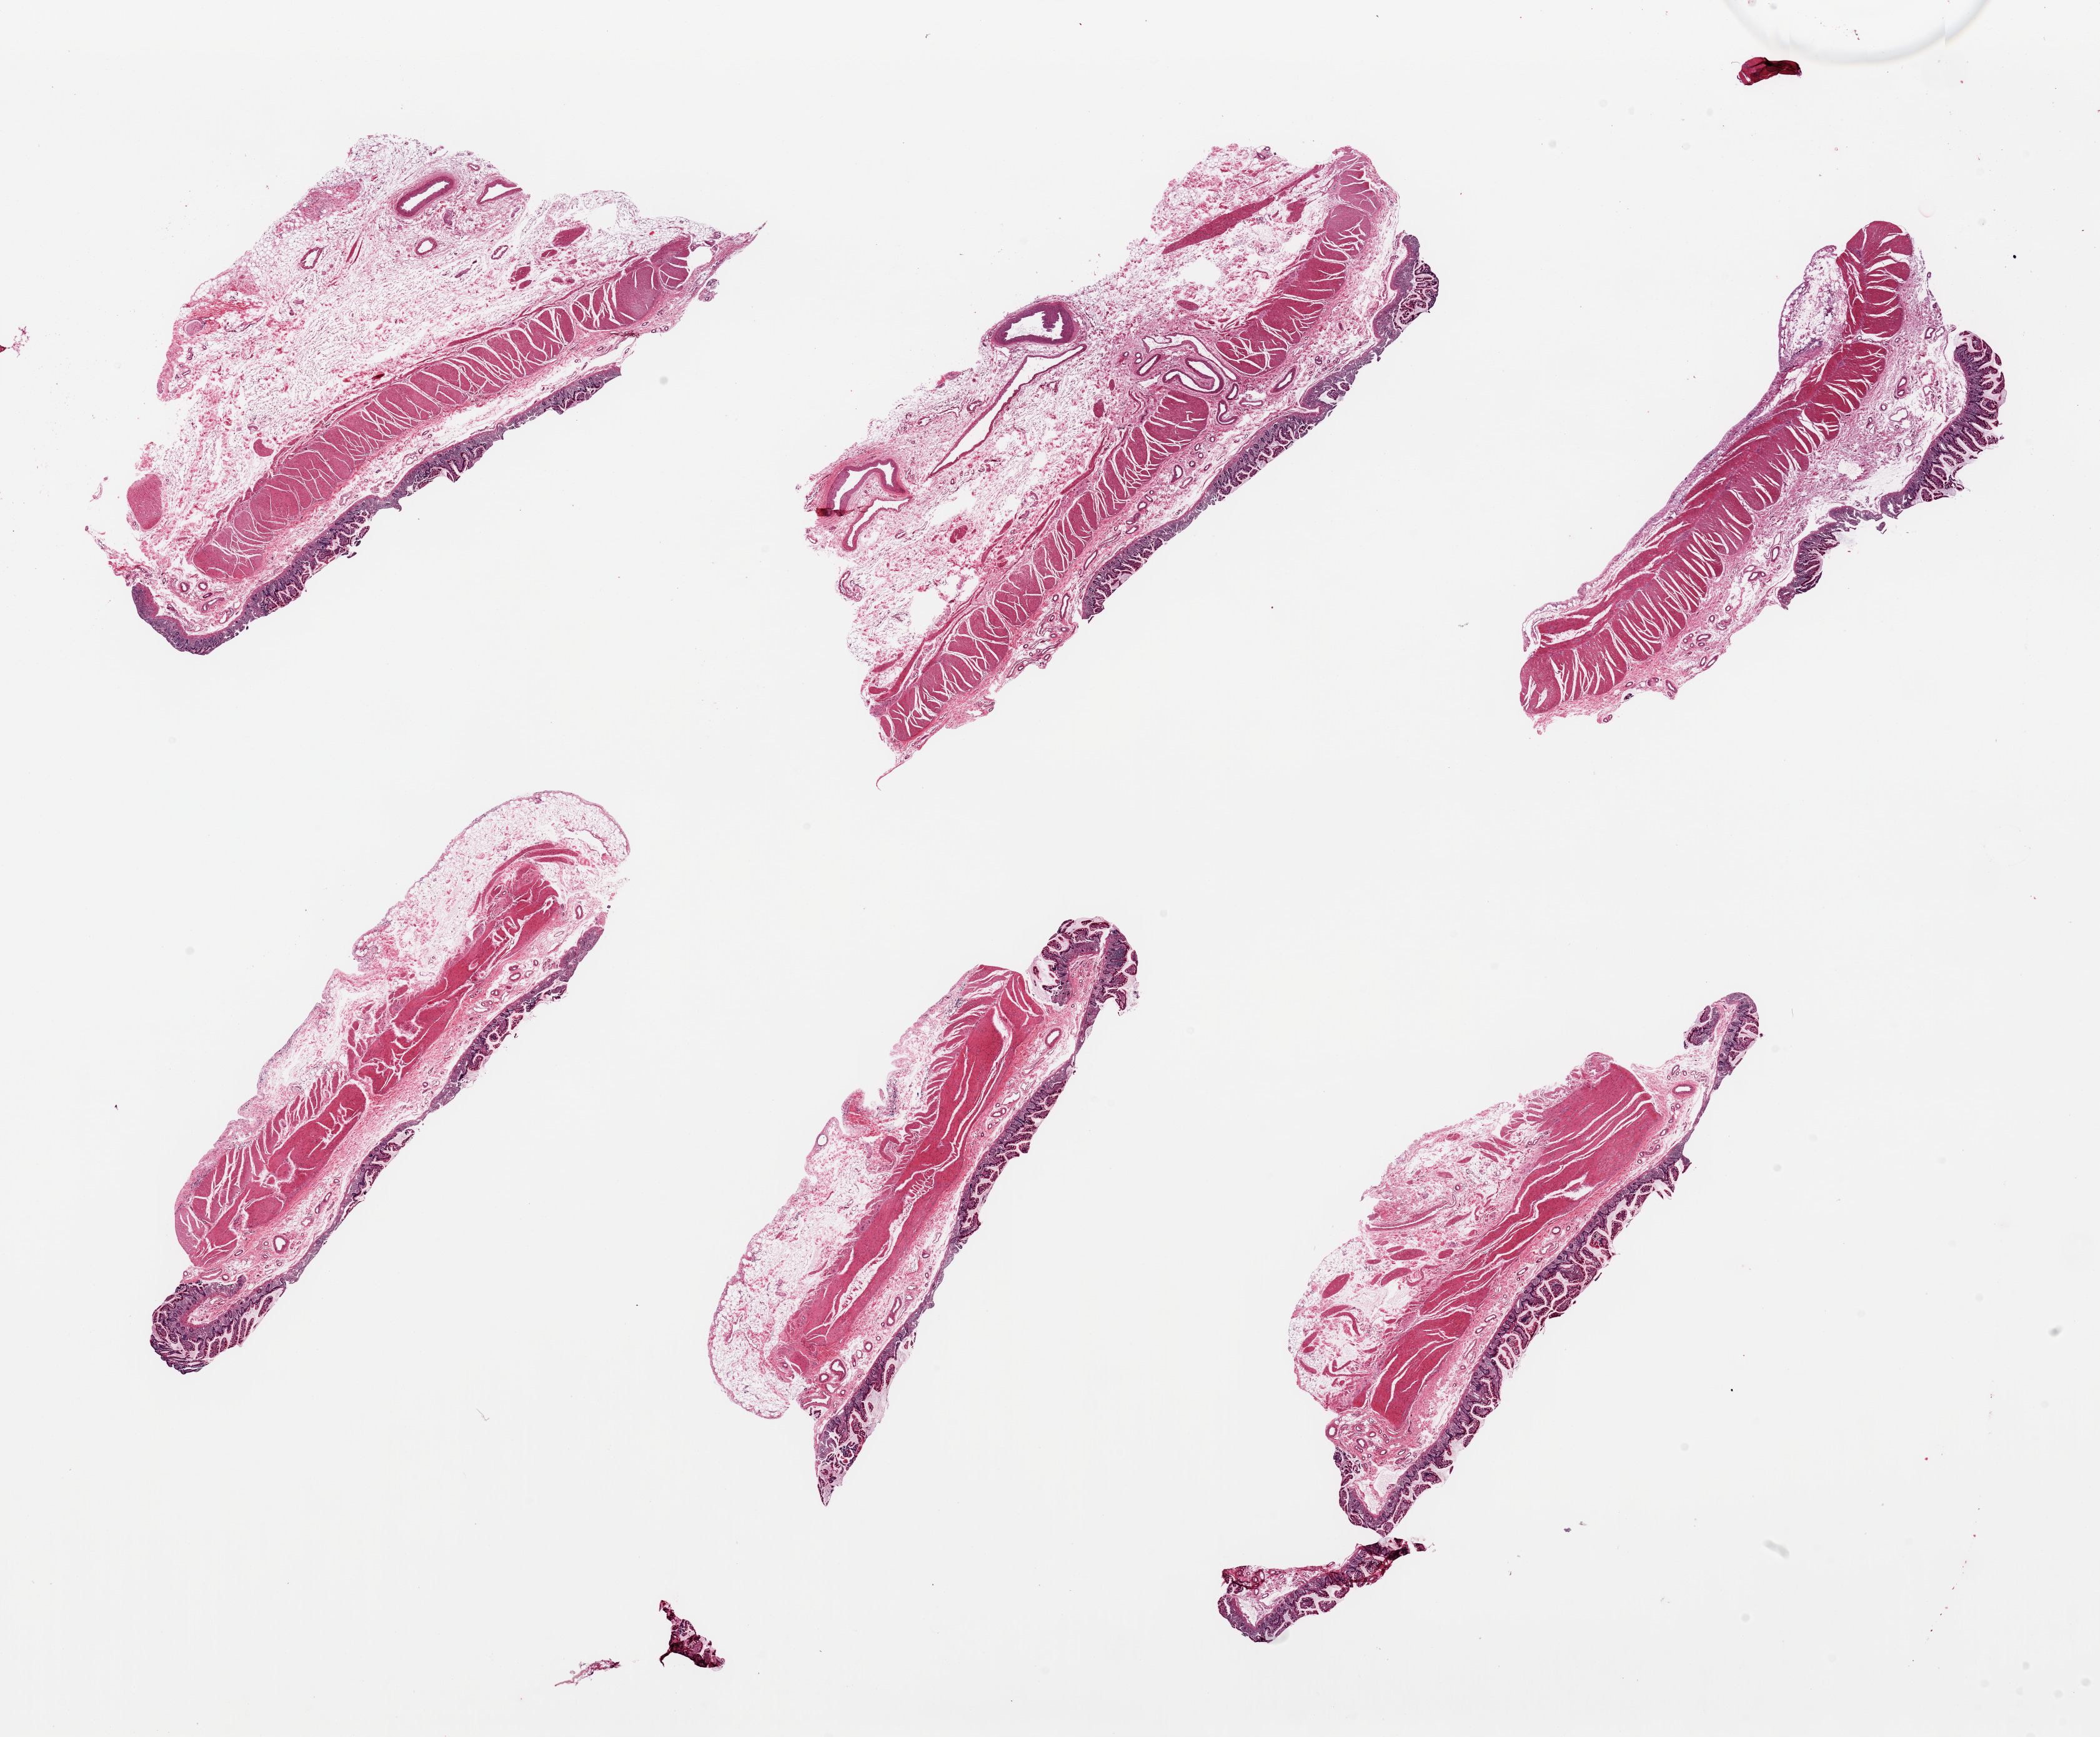
Digitized haematoxylin and eosin-stained section, whole scanned area (about 26.6 x 22.0 mm, from a 20x scan) shown as a low-resolution overview; PAXgene-fixed paraffin-embedded (PFPE) section; section of ileum (target tissue); tissue donor sample.
Pathologist's review note for this sample: 6 pieces, no target lymphoid aggregates present.